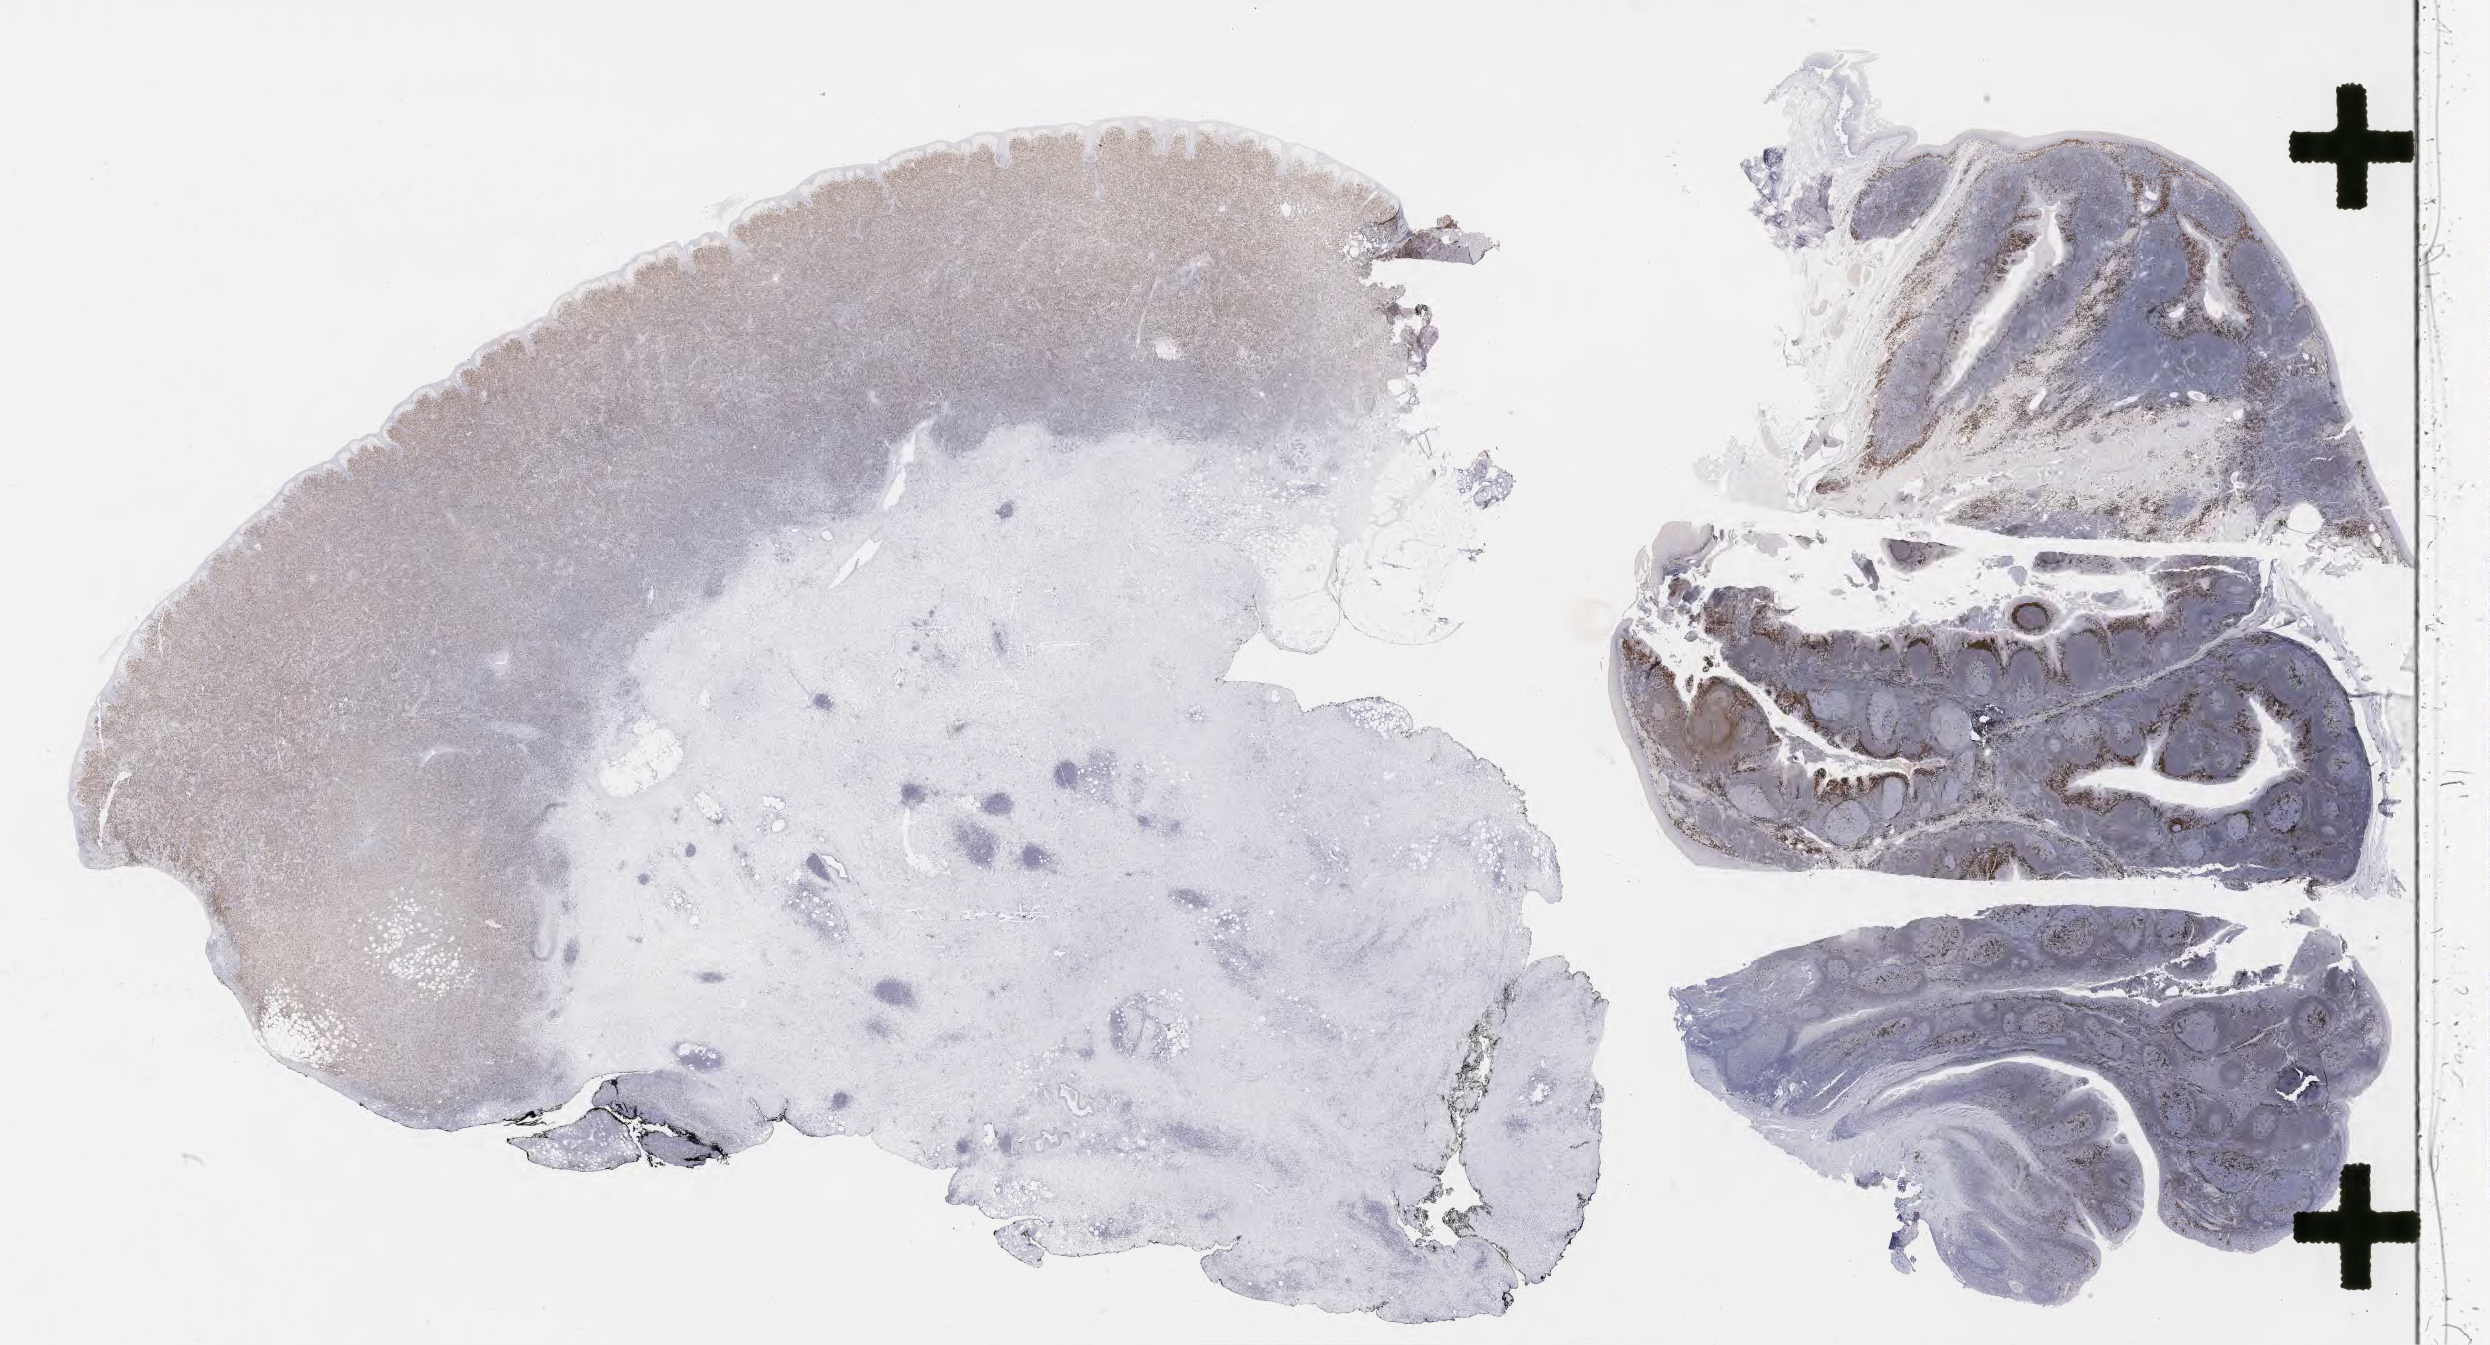
Whole-slide image, immunohistochemical stain for IRF4/MUM1, low-resolution overview of the scanned area, about 40.2 x 21.7 mm, tumor tissue, anatomic site: lymph node. Patient: male, age 52 years.
* diagnosis: Diffuse large B-cell lymphoma, NOS